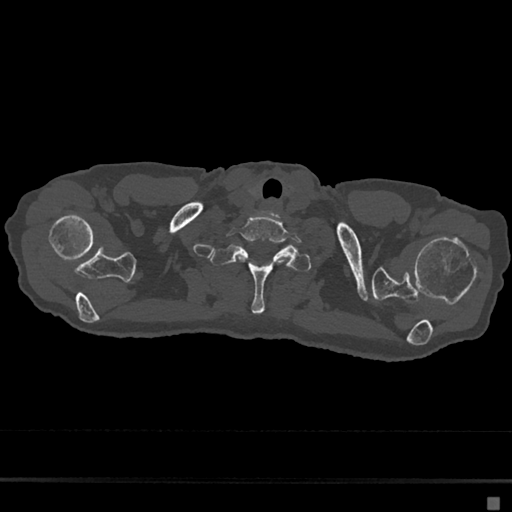
CT including the spine, one axial slice; position 623 of 797 along the scan axis; 120 kVp; bone window (W 1800 / L 400 HU); 512 × 512 image matrix, field of view 360 × 360 mm. Patient: female, 68 years. Case-level facts recorded for this patient, not image findings: primary cancer: renal.
Annotated regions visible in this slice (semi-automatic segmentation, software-assisted and operator-edited):
- T1 vertebra: box from (x=210, y=245) to (x=312, y=314) px